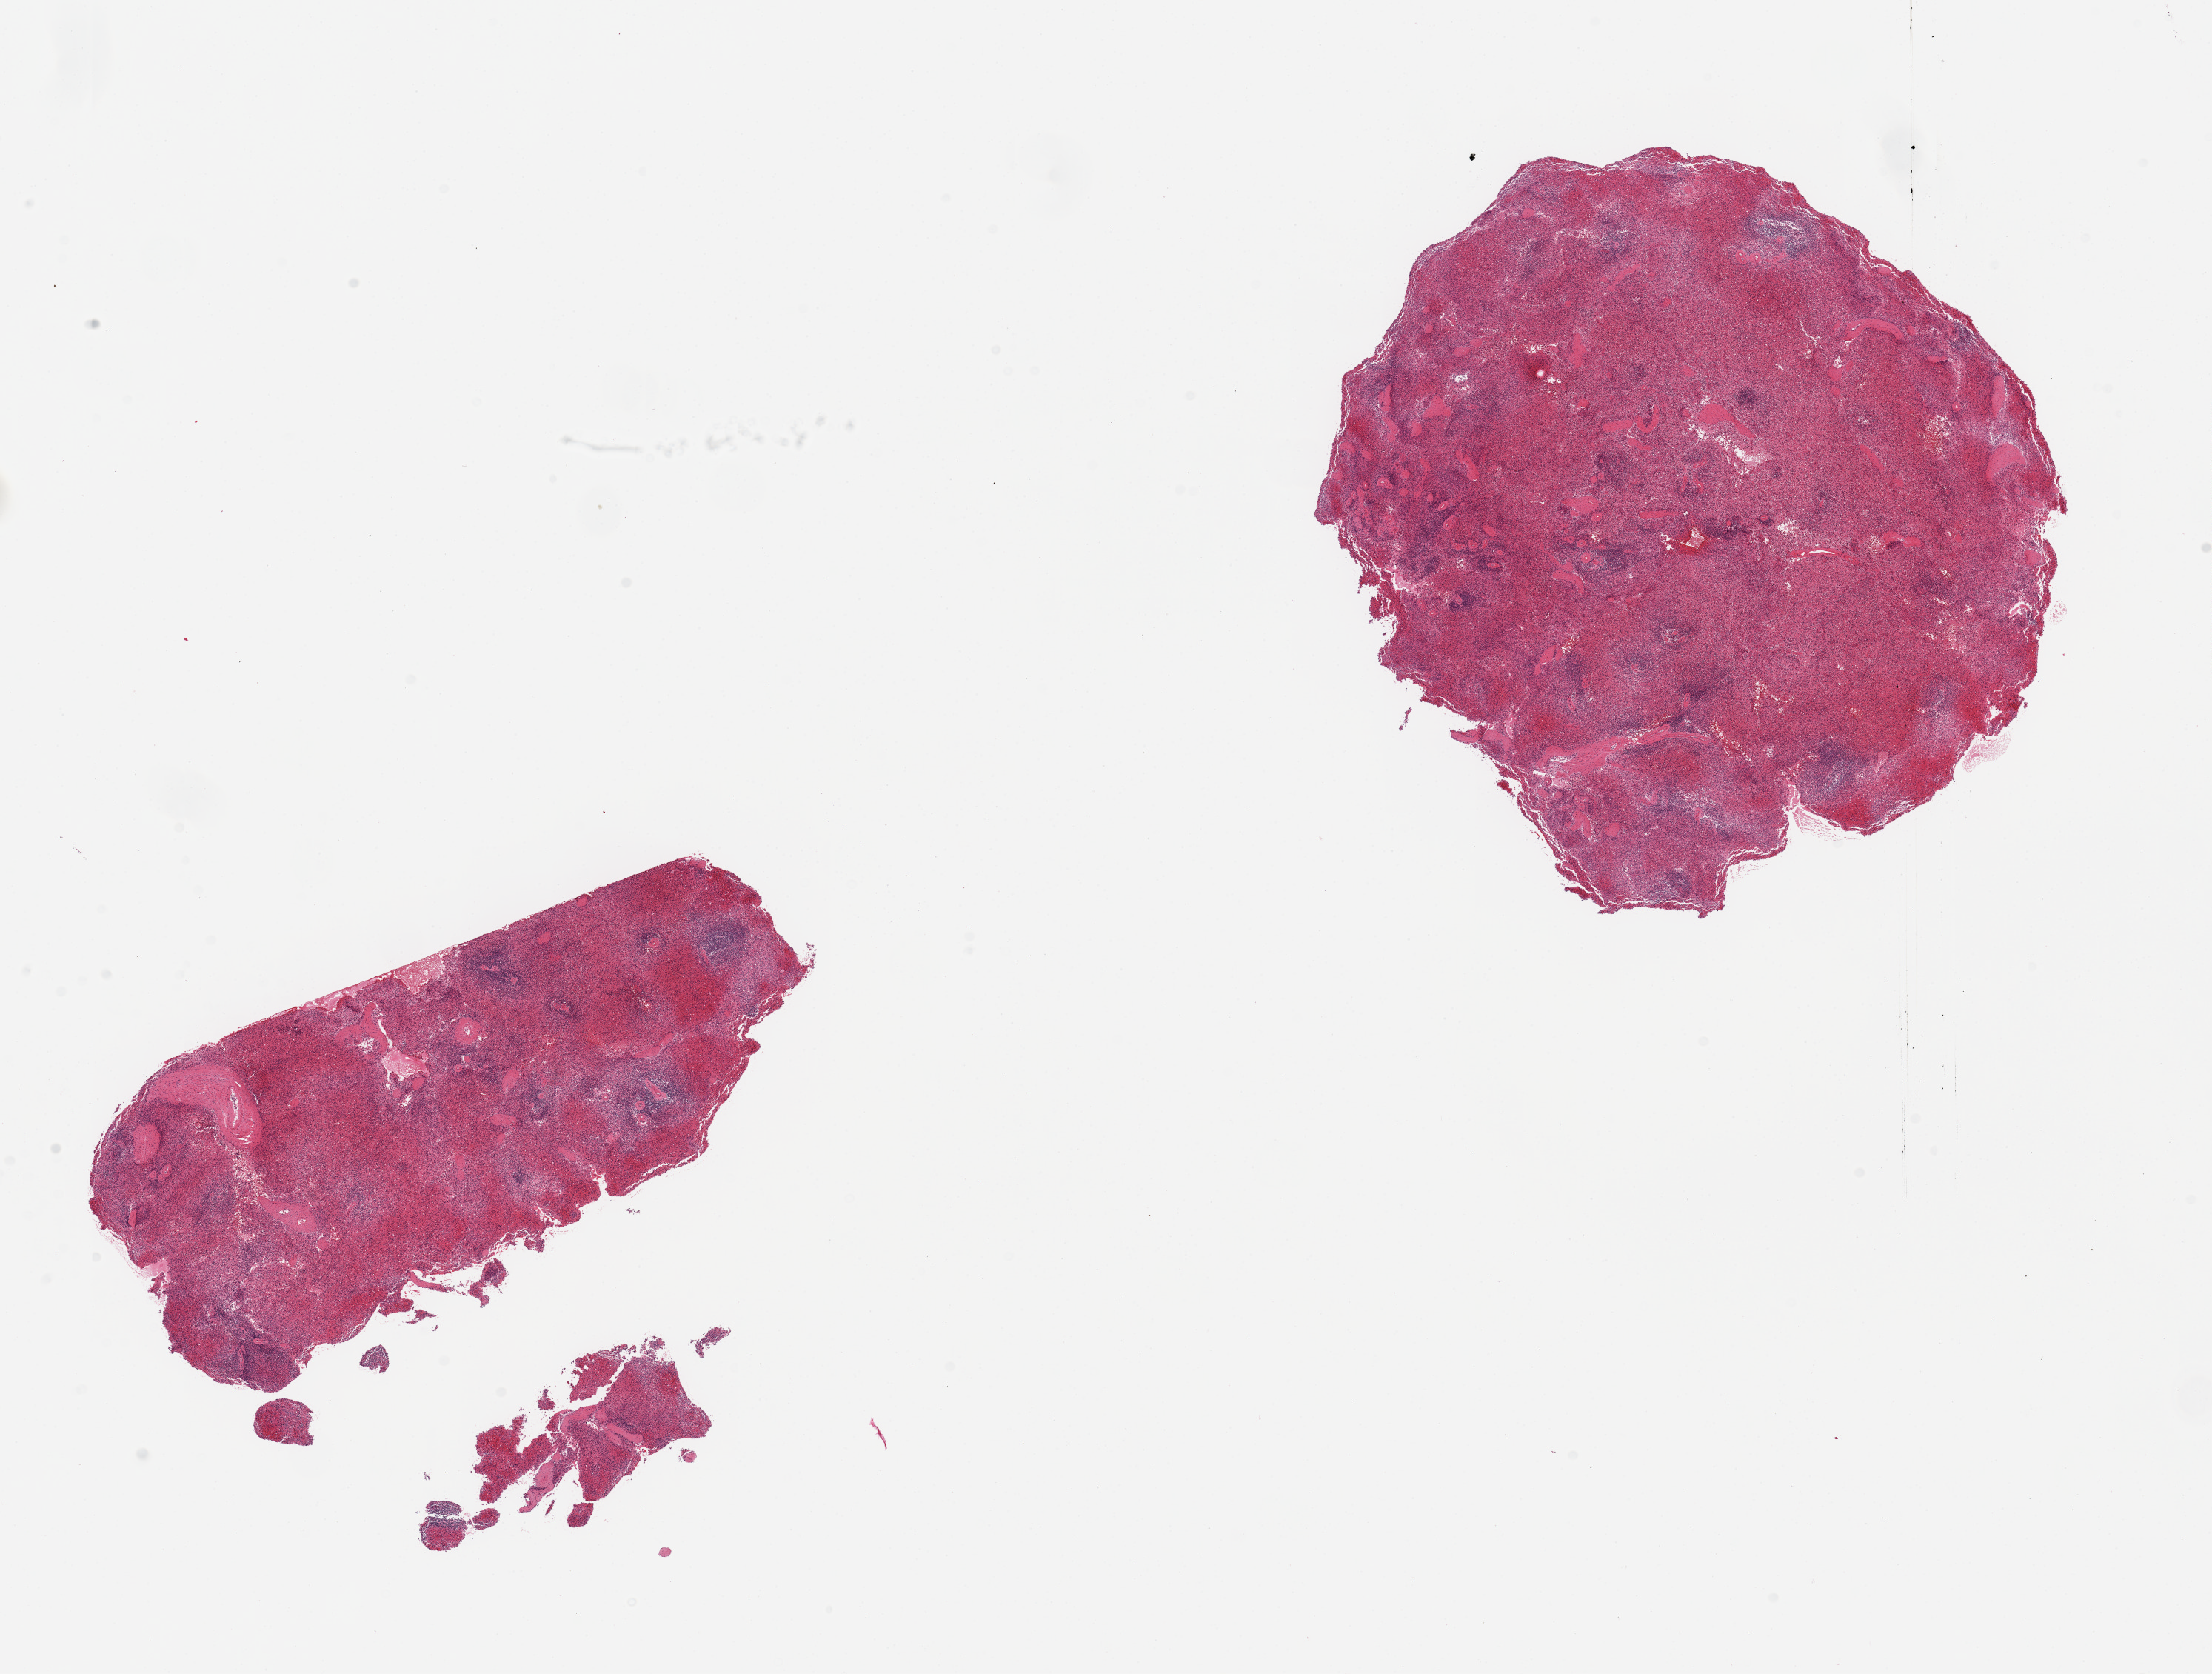
Whole-slide image, H&E stain — a low-resolution overview of the entire scanned area, about 23.6 x 17.9 mm, PAXgene-fixed paraffin-embedded (PFPE) section, section of spleen (target tissue), donor tissue sample. Donor: female.
• review note (as recorded): 2 pieces, moderate congestion